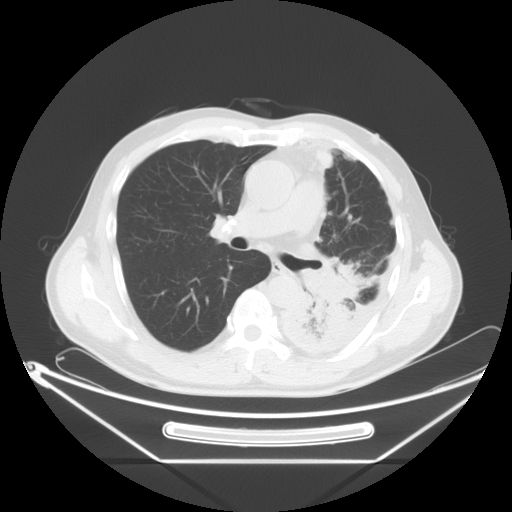
Chest CT, one axial slice. Position 37 of 63 along the scan axis. Reconstruction kernel STANDARD. 120 kVp. Lung window (W 1500 / L -600 HU). 5 mm slice thickness. 512 × 512 image matrix, field of view 442 × 442 mm. Male patient, age 60 years. Case-level facts recorded for this patient, not image findings: clinical TNM (as recorded): T4 N1 M1.
Annotated regions visible in this slice (rectangle marked by the reading radiologist):
- lung tumour (recorded histology: adenocarcinoma): bounding box (x1, y1, x2, y2) in pixels: (295, 238, 375, 335)